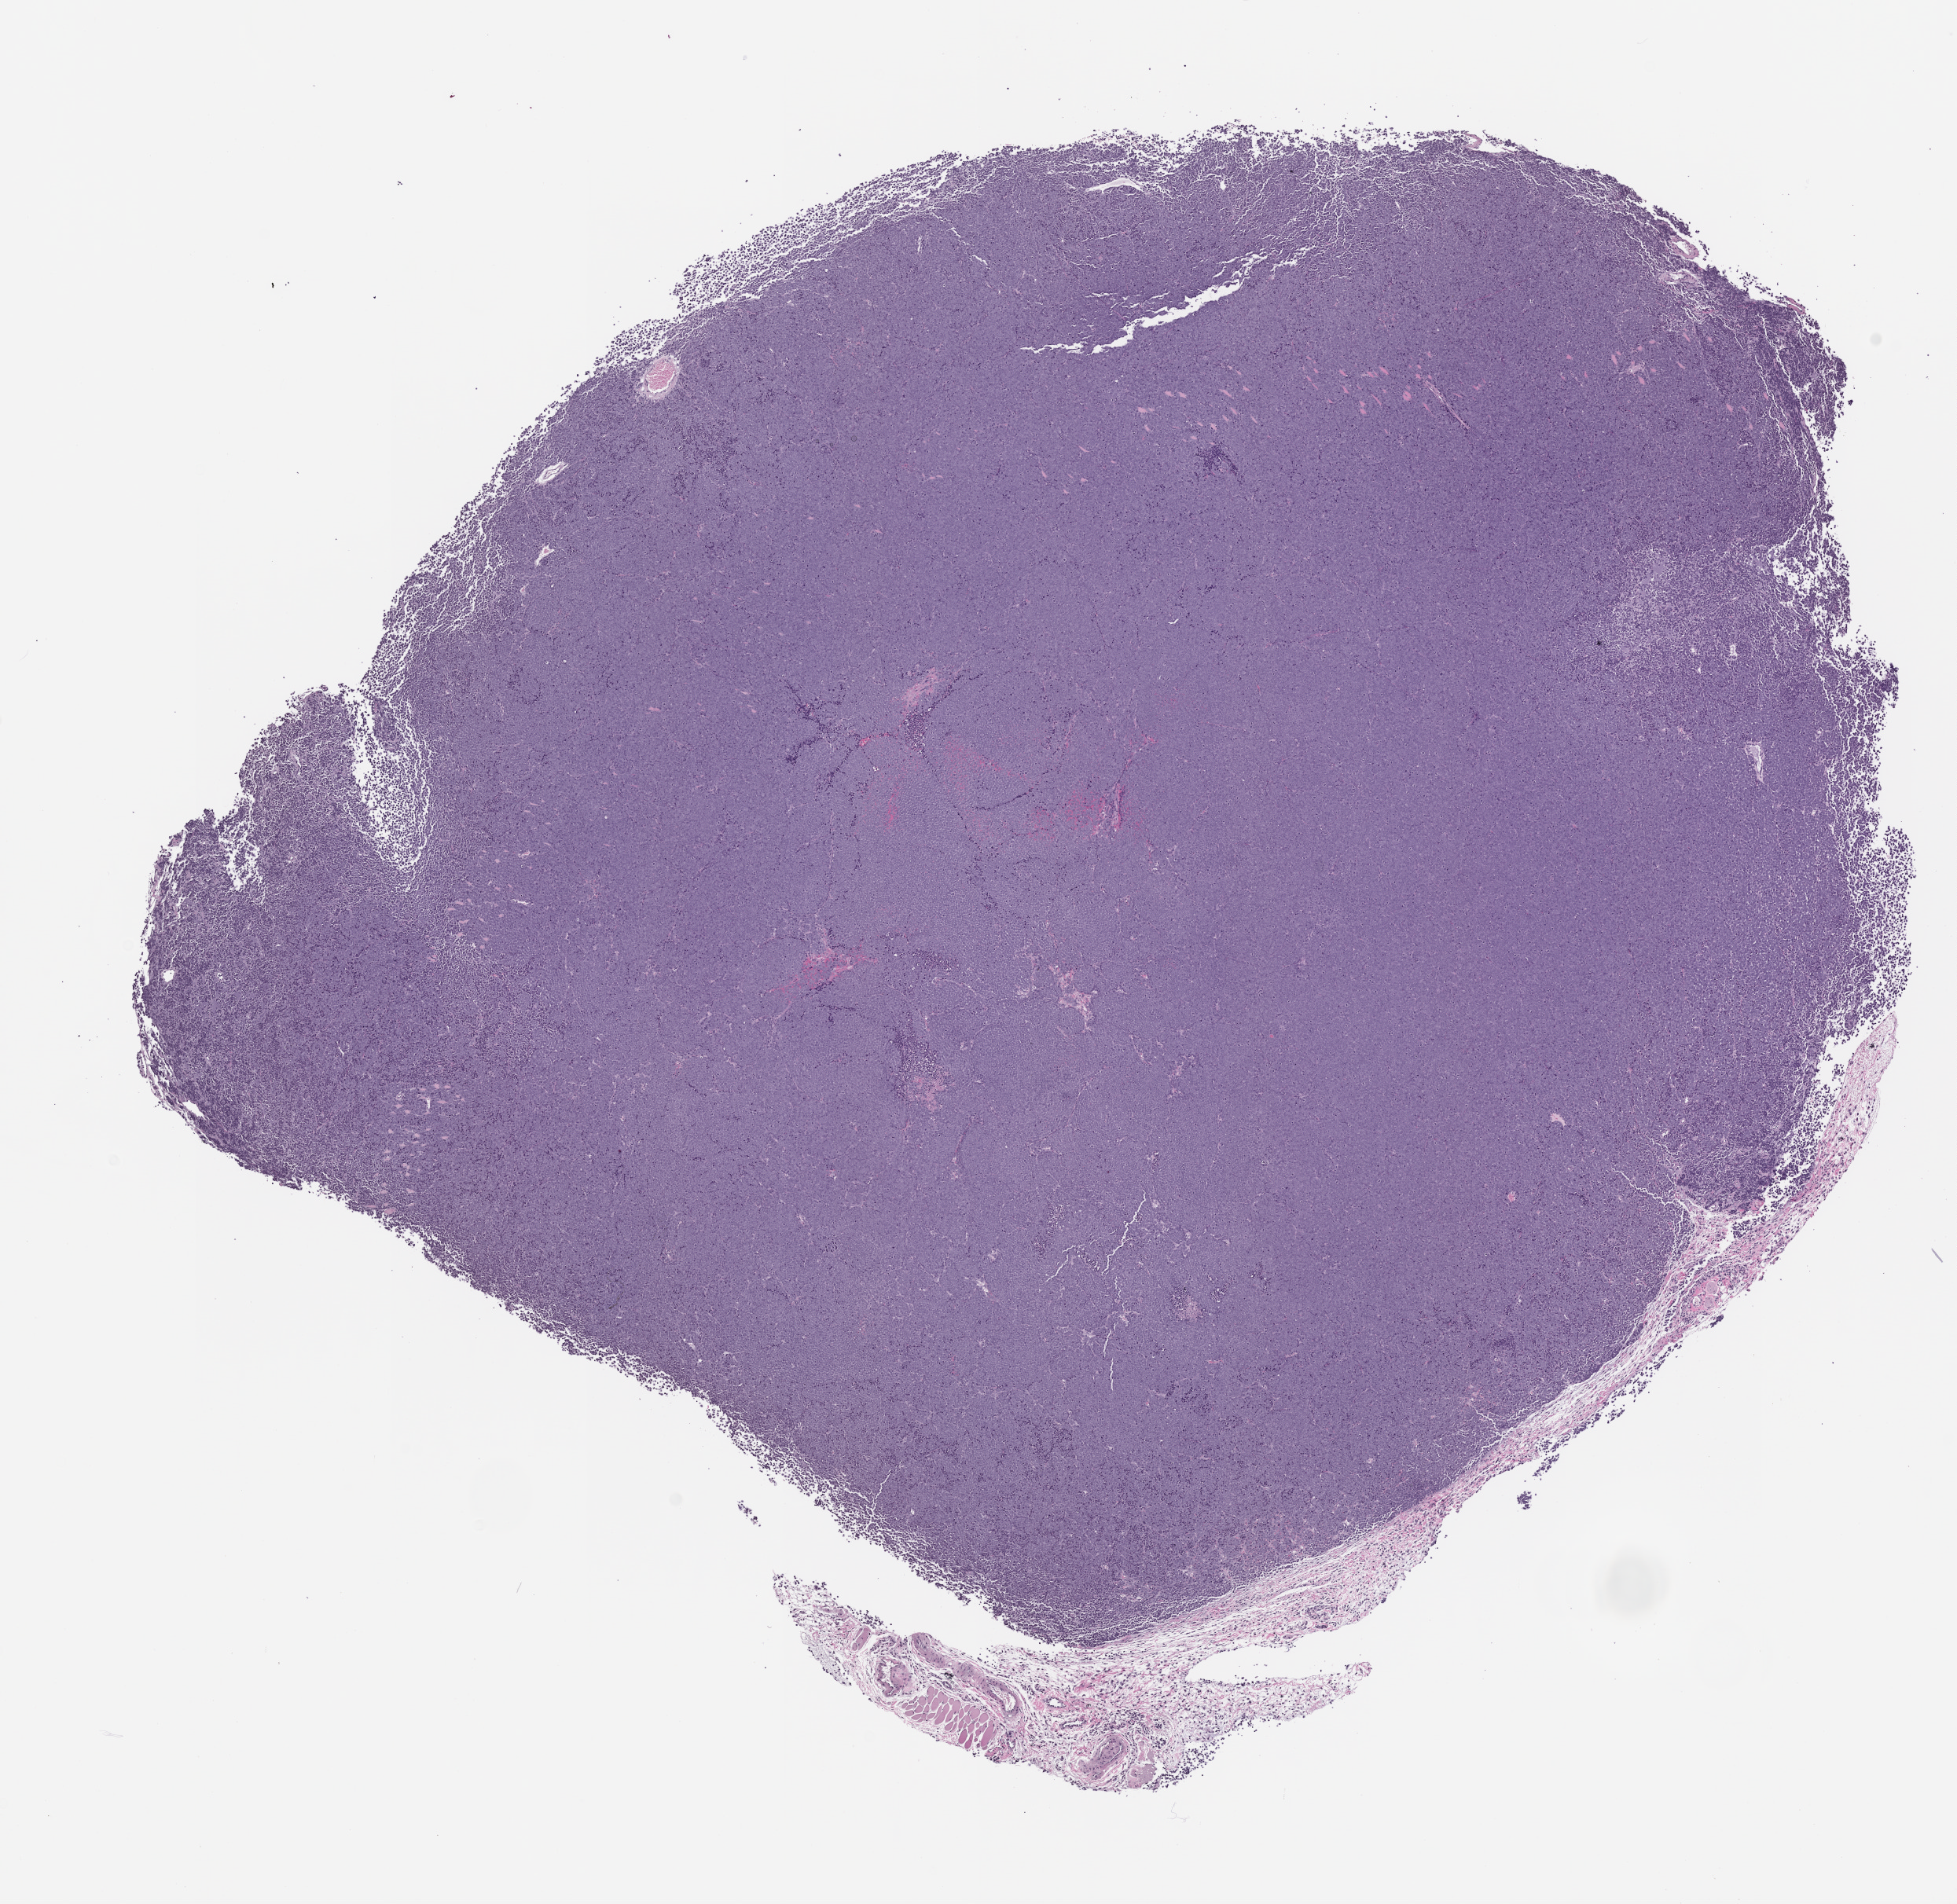
Whole-slide image, haematoxylin and eosin: patient-derived xenograft (human tumor grown in a mouse) — whole scanned area (about 10.0 x 9.7 mm) shown as a low-resolution overview. FFPE section. Originating tumor site category: endocrine.
Originating patient diagnosis: Merkel Cell Carcinoma.